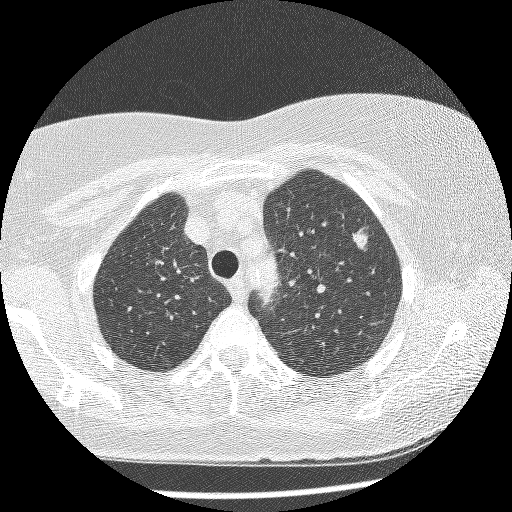
Low-dose screening chest CT, axial slice. Baseline screening round. Lung window (W 1500 / L -600 HU). Lung (sharp) reconstruction kernel (BONE). 120 kVp. Slice 184 of 241 in the series. Female, age 61 years at enrolment.
Expert reader's lesion annotation, bounding box (x1, y1, x2, y2) in pixels: (329, 220, 383, 269). The screening reader recorded 4 non-calcified nodules or masses ≥4 mm on this exam; which of them this box marks is not recorded. Participant outcome: lung cancer diagnosed 111 days after this screen — bronchiolo-alveolar adenocarcinoma, NOS, left upper lobe, stage IV (AJCC 6th edition), 10 mm at pathology.